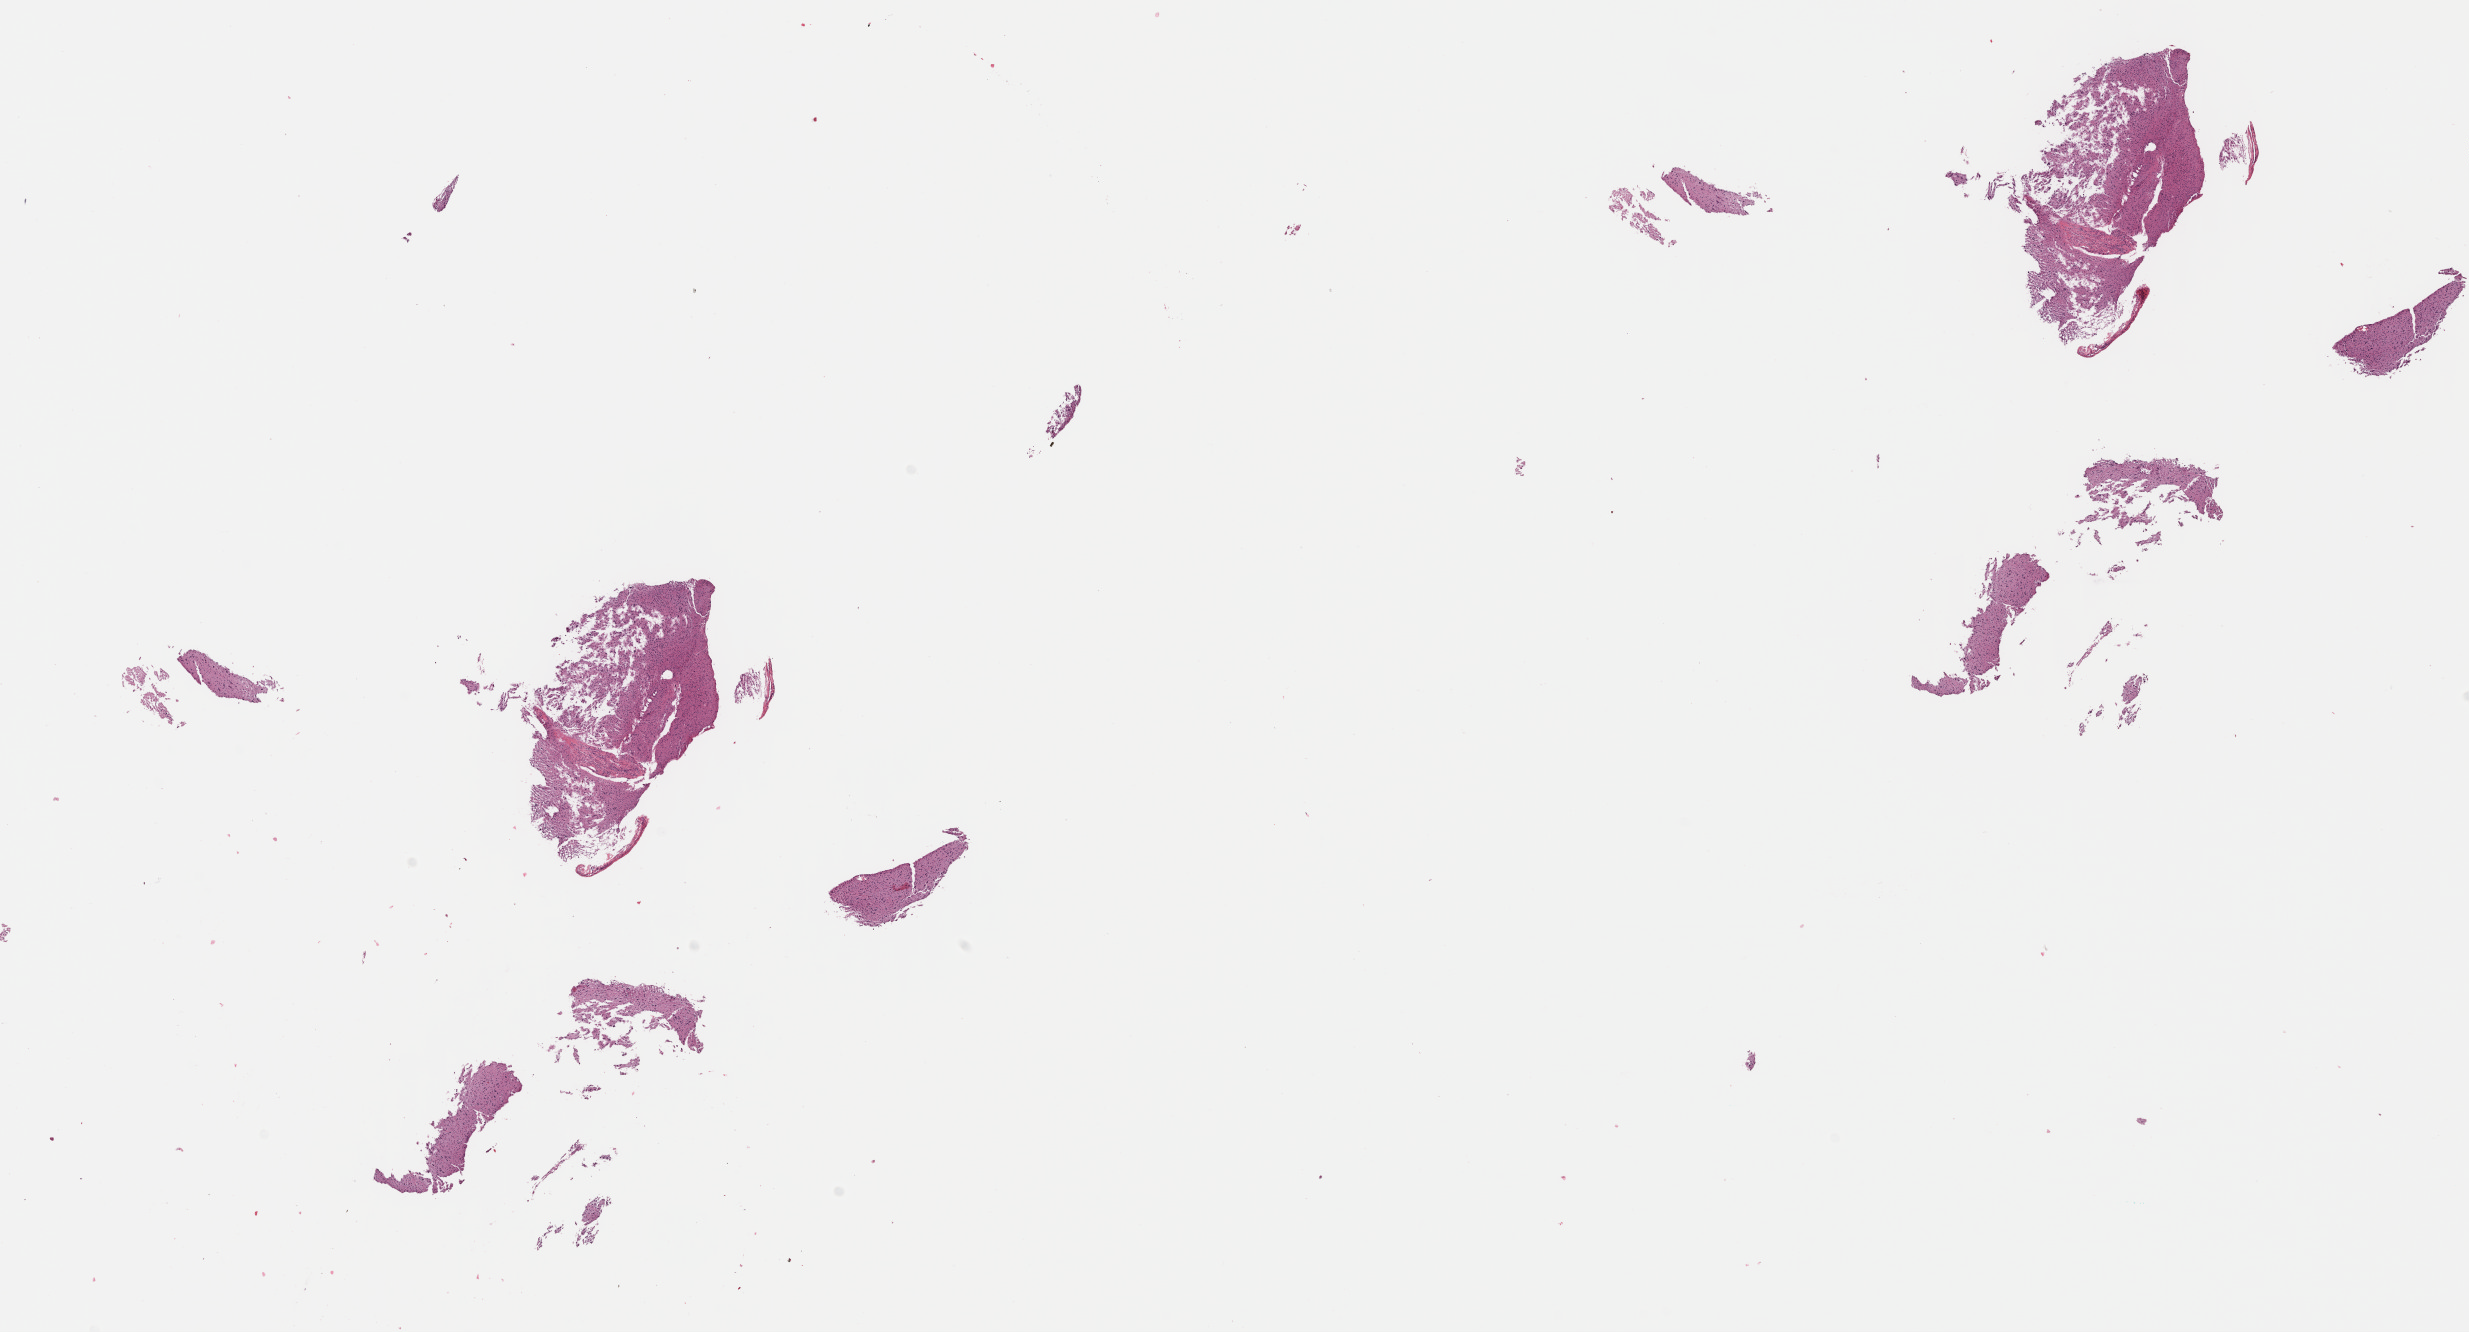
Digitized H&E-stained tissue section (whole slide), whole scanned area (about 19.4 x 10.5 mm) shown as a low-resolution overview; formalin-fixed paraffin-embedded (FFPE) diagnostic section; brain, primary tumour sample. Male patient; age at initial diagnosis 56 years. Histologic grade: G2 (moderately differentiated).
Laterality: left. Histologic diagnosis: Oligodendroglioma, NOS.